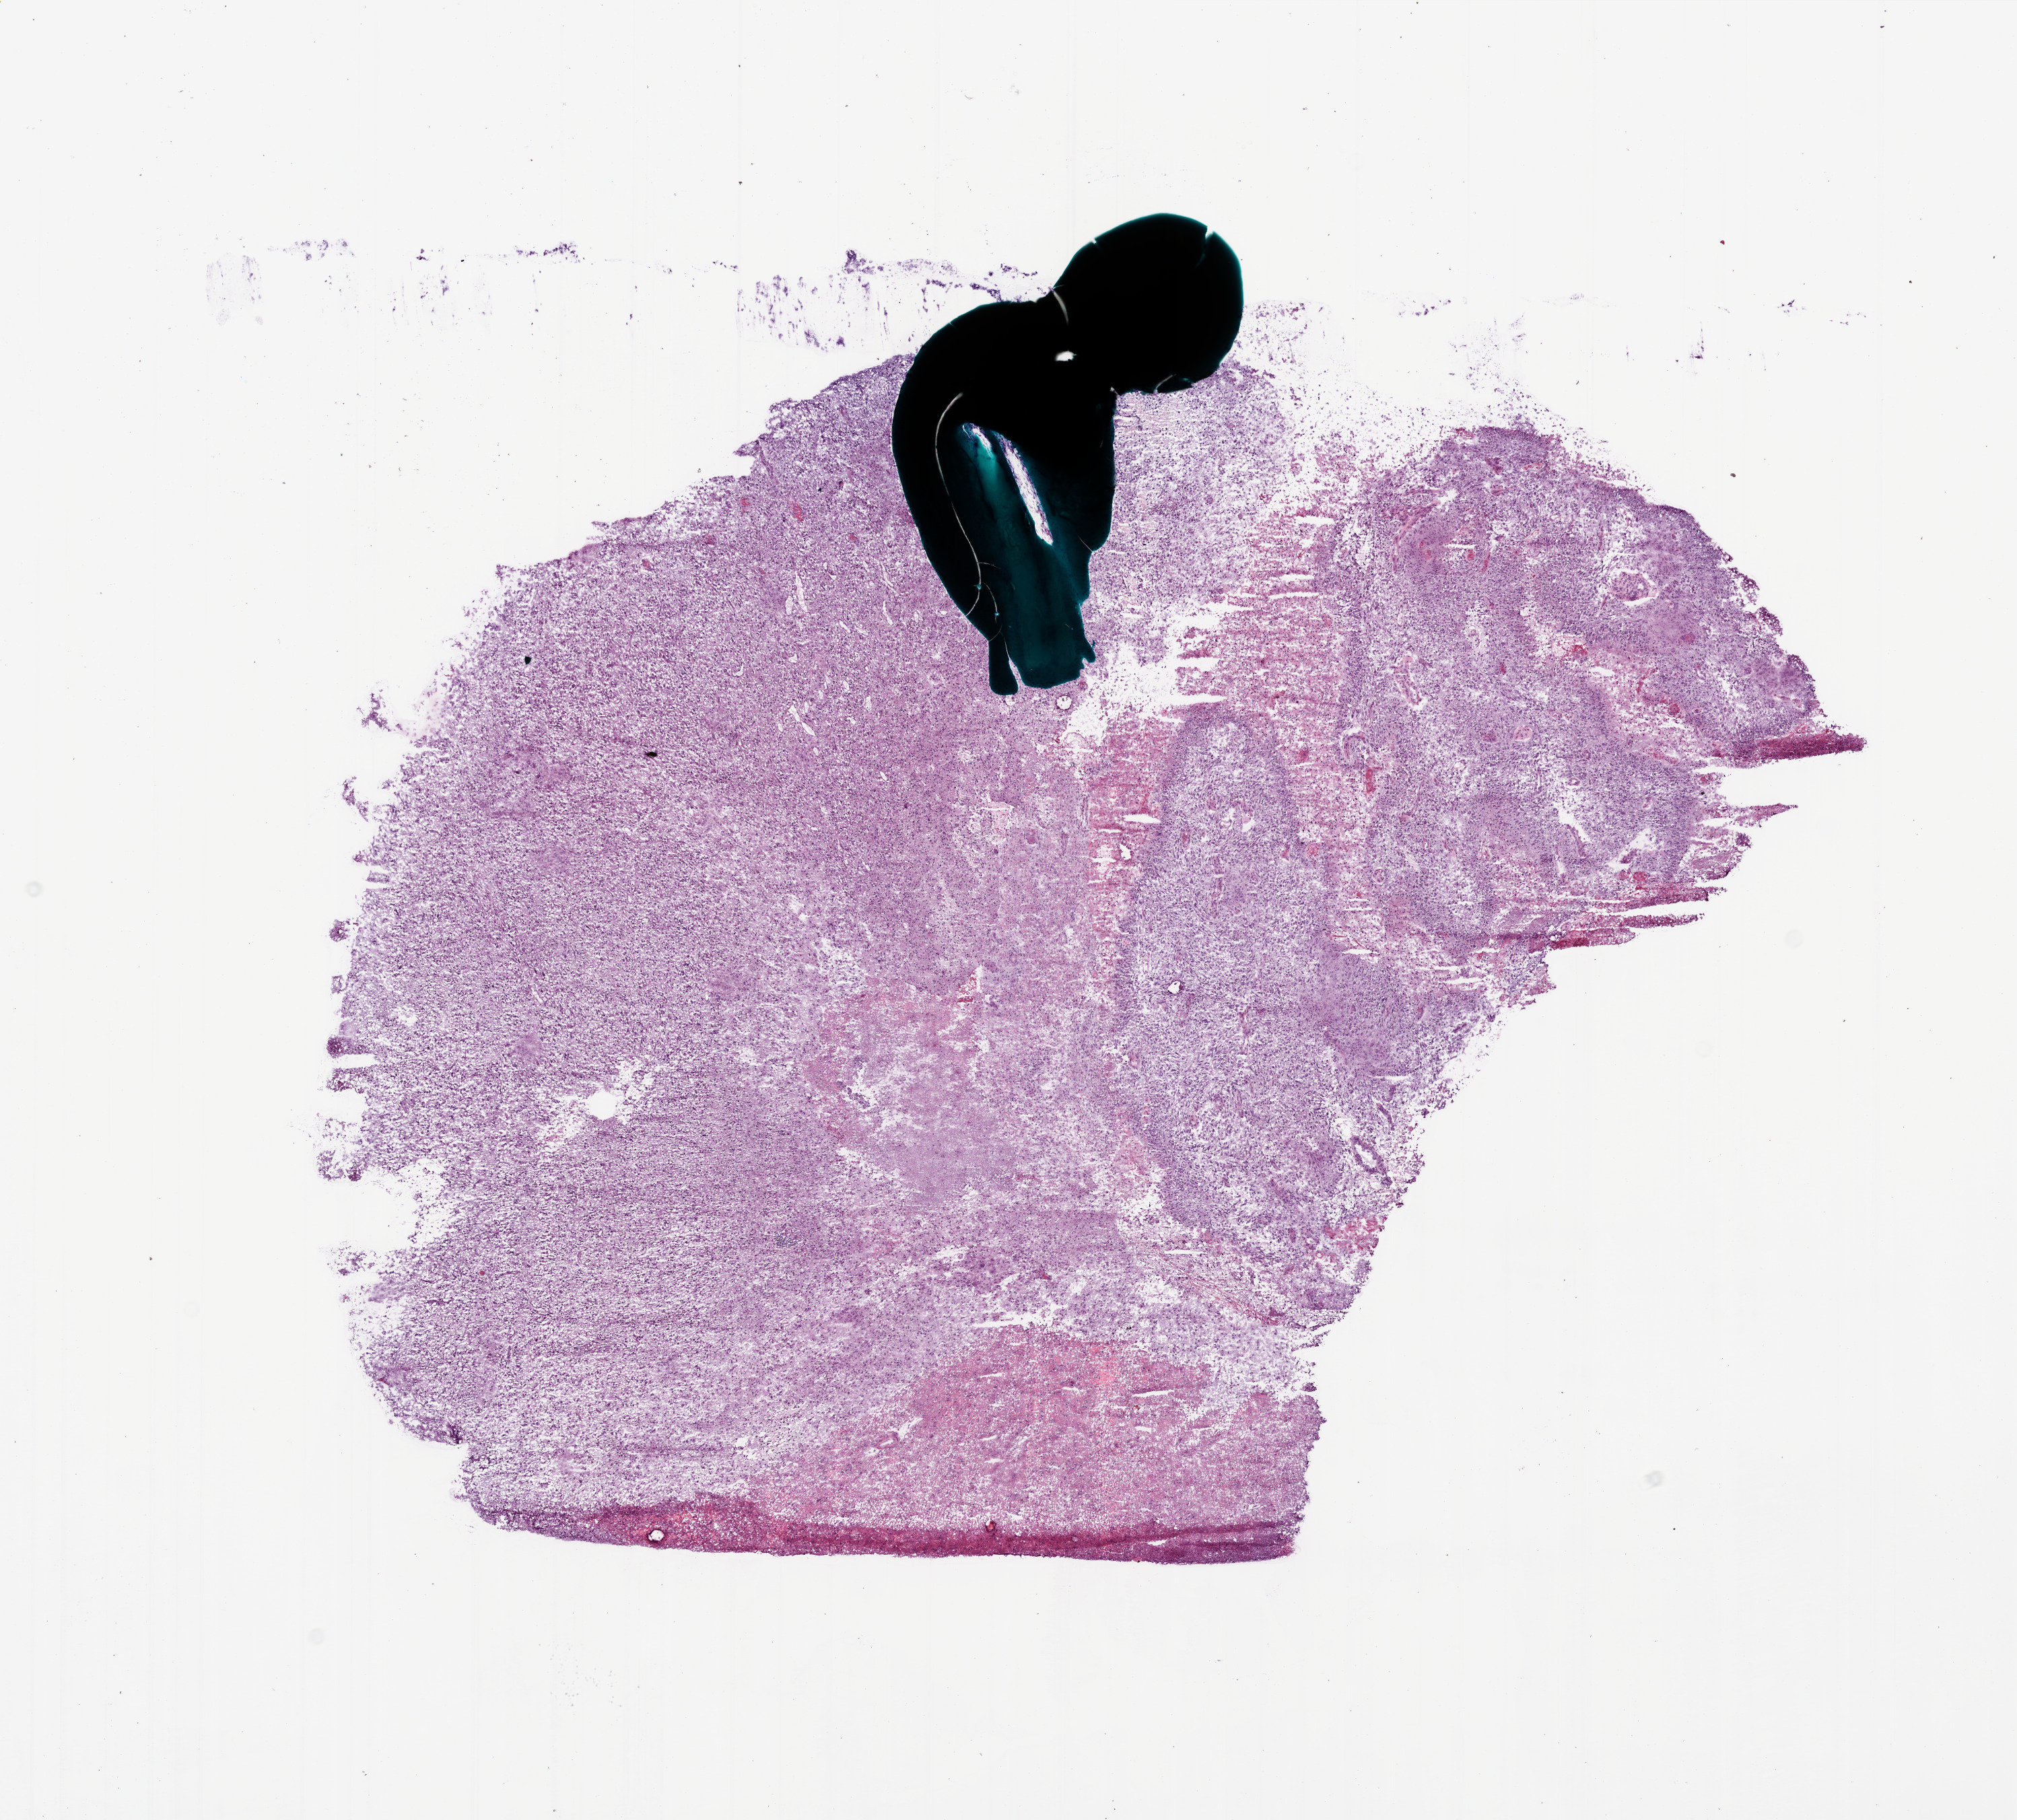
Hematoxylin and eosin (H&E) stained whole-slide image — a low-resolution overview of the entire scanned area, about 12.0 x 10.8 mm. Frozen section. Brain, primary tumour sample. Patient: male, age at initial diagnosis 30 years. Slide review estimates, as recorded: tumour cells 80%, tumour nuclei 80%, normal cells 0%, stromal cells 0%, necrosis 20%.
- histologic diagnosis: Glioblastoma